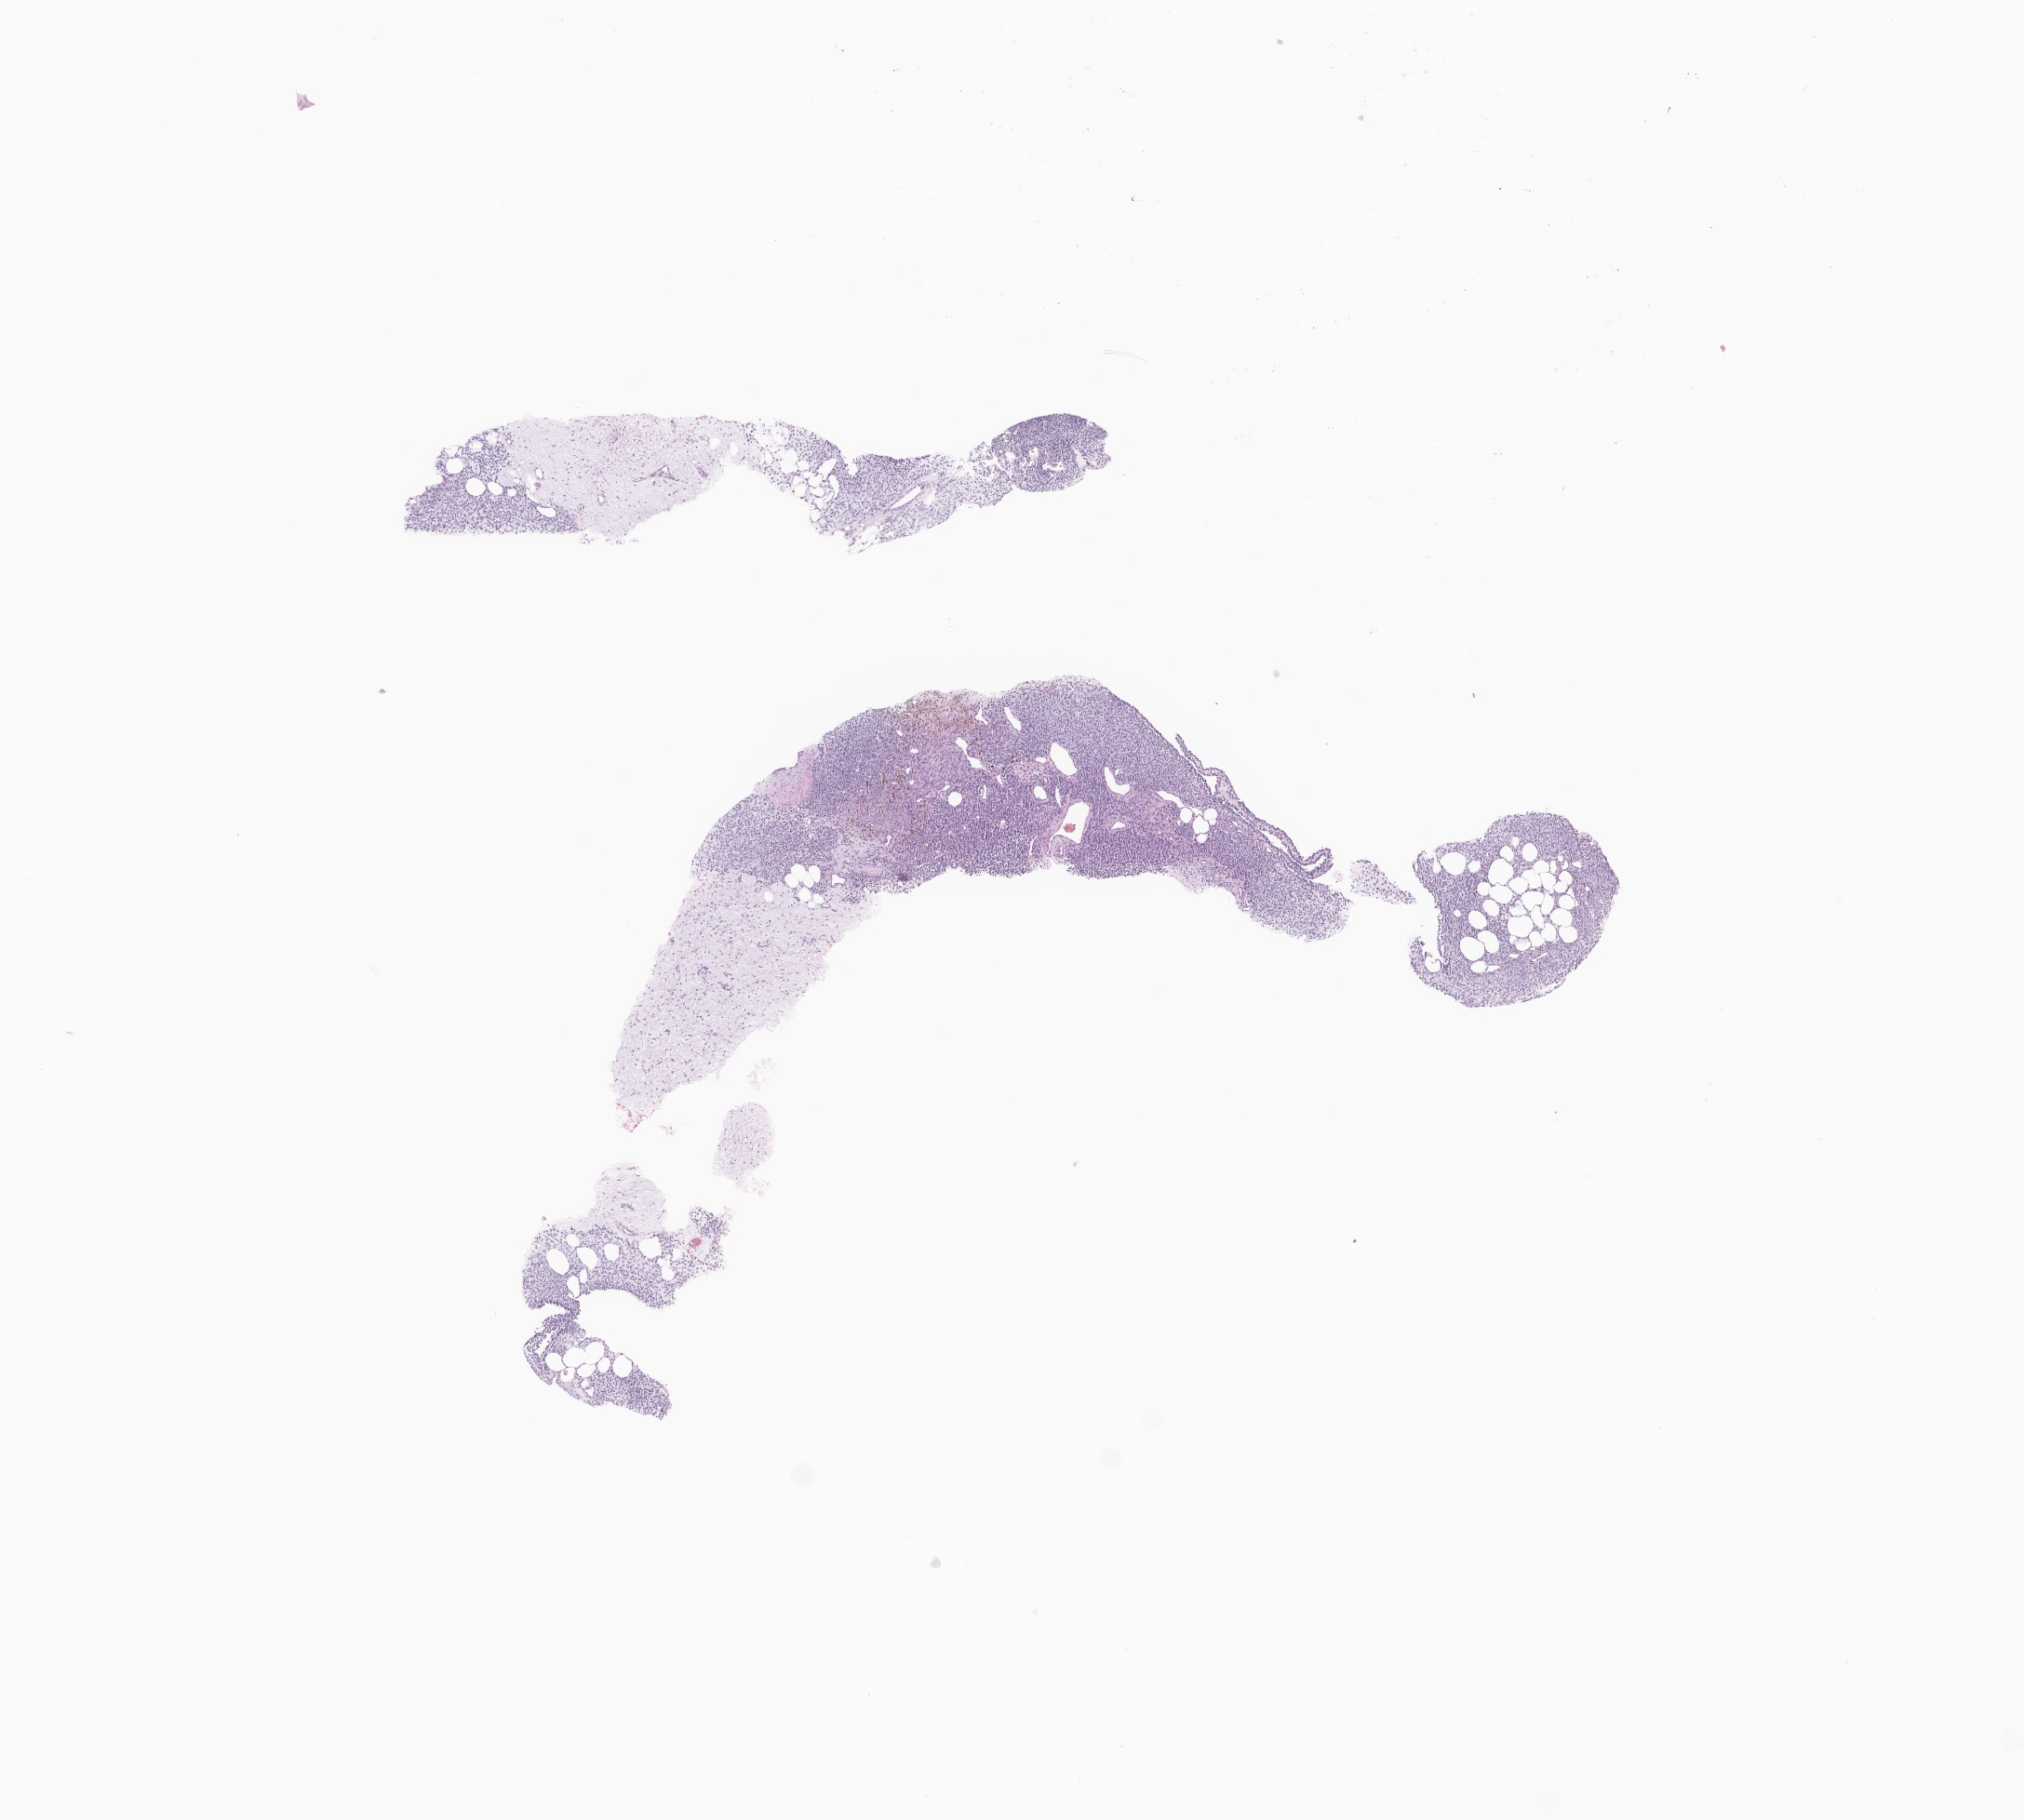
H&E whole-slide image of tumor tissue from the soft tissue of lower extremity — whole scanned area (about 9.2 x 8.2 mm) shown as a low-resolution overview. Formalin-fixed paraffin-embedded section. Patient: male, age 348 days.
- recorded diagnosis: Infantile fibrosarcoma